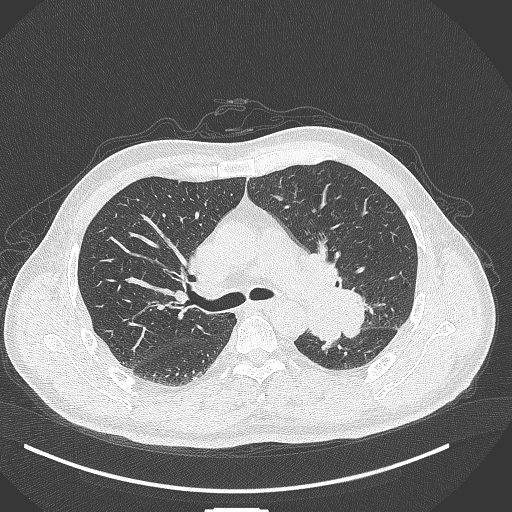
Chest CT, one axial slice. Slice 267 of 429 in the series (ordered by position). Lung window (W 1500 / L -600 HU). 1 mm slice thickness. 512 × 512 image matrix, field of view 400 × 400 mm. Male patient, age 55 years. From the clinical record (not read from this slice): clinical TNM (as recorded): T3 N0 M1c; histopathological grade: G3.
Structures marked on this image (rectangle marked by the reading radiologist):
- lung tumour (recorded histology: adenocarcinoma): bounding box (x1, y1, x2, y2) in pixels: (308, 275, 374, 346)